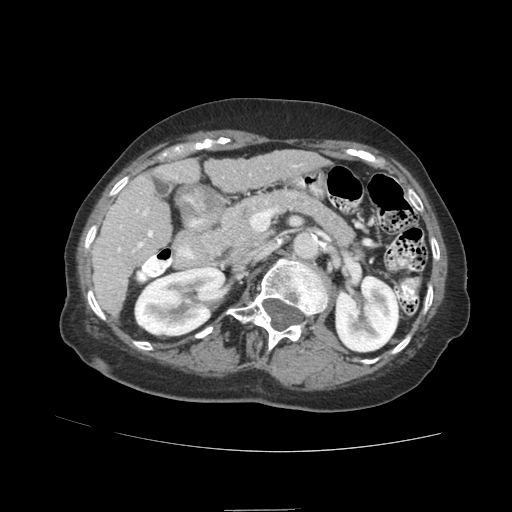
Contrast-enhanced abdominal CT (liver protocol), one axial slice; 140 kVp; soft-tissue window (W 400 / L 40 HU); 2.5 mm slice thickness; 512 × 512 image matrix, field of view 360 × 360 mm. From the clinical record (not read from this slice): diagnosis: hepatocellular carcinoma (patient treated with transarterial chemoembolisation; whether this scan precedes or follows treatment is not stated here); TNM stage (as recorded): Stage-II; Child-Pugh class: A; tumour differentiation: moderately differentiated; tumour nodularity: multinodular.
Annotated regions visible in this slice (semi-automatically segmented with operator editing):
- liver parenchyma outside the tumour (the mass and vessels are separate outlines, so this box may not span the whole liver): bounding box (x1, y1, x2, y2) in pixels: (92, 150, 326, 316)
- liver vessels: (109, 165, 296, 289)